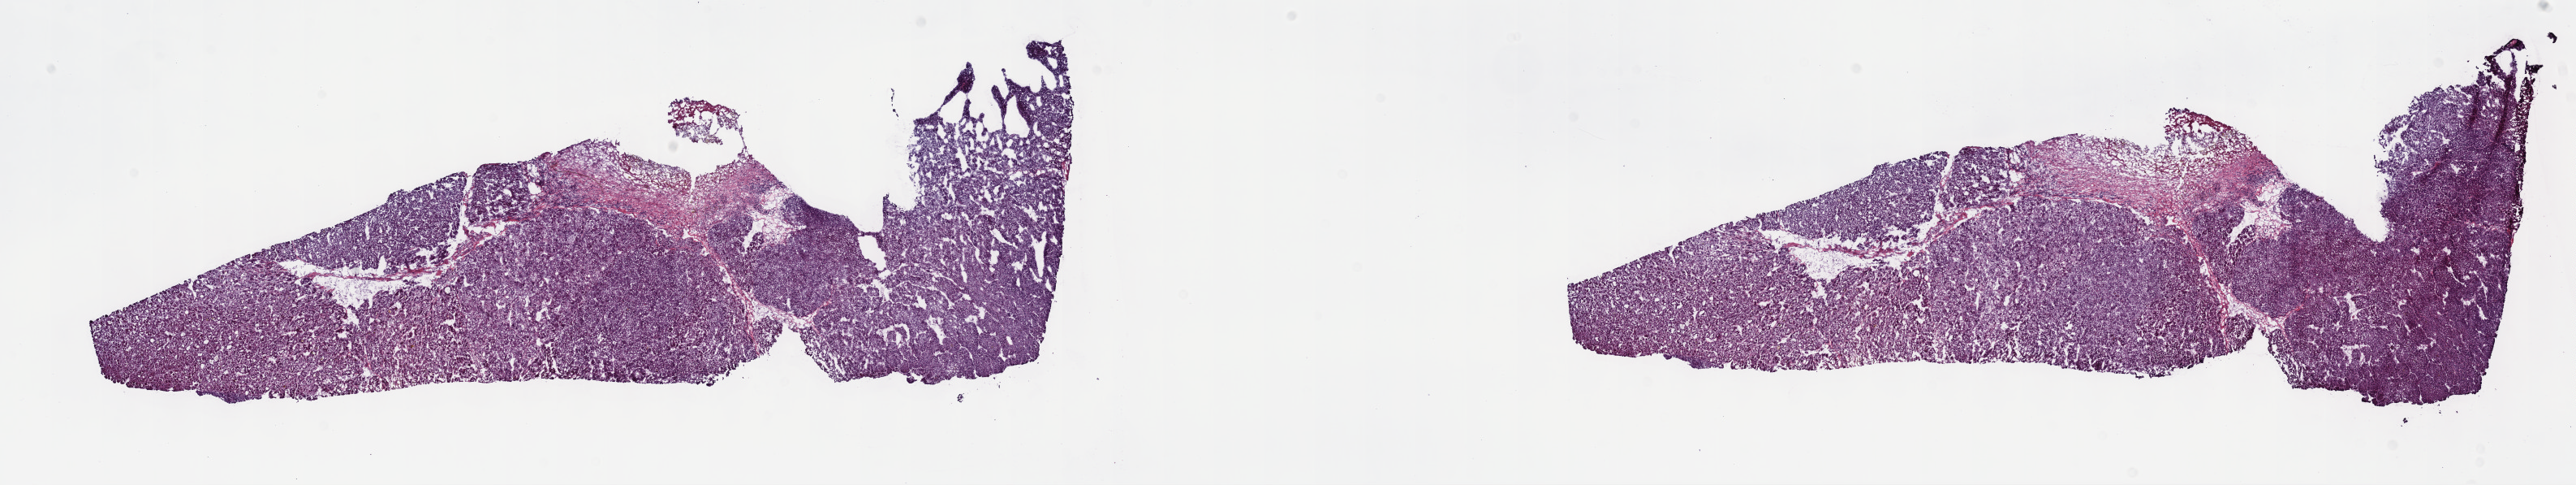
Whole-slide histology image, H&E-stained, whole scanned area (about 25.7 x 4.8 mm, slide scanned at 40x) shown as a low-resolution overview, frozen section from the top of the tissue portion, liver, primary tumour sample. Male patient; age at initial diagnosis 70 years. Histologic grade: G2 (moderately differentiated). Composition of this section per pathologist review: tumour cells 89%, tumour nuclei 95%, normal cells 0%, stromal cells 8%, necrosis 3%. Inflammatory infiltration, as recorded: lymphocyte infiltration 4%, monocyte infiltration 0%, neutrophil infiltration 1%.
AJCC pathologic stage: II (7th edition). Histologic diagnosis: Hepatocellular carcinoma, NOS.